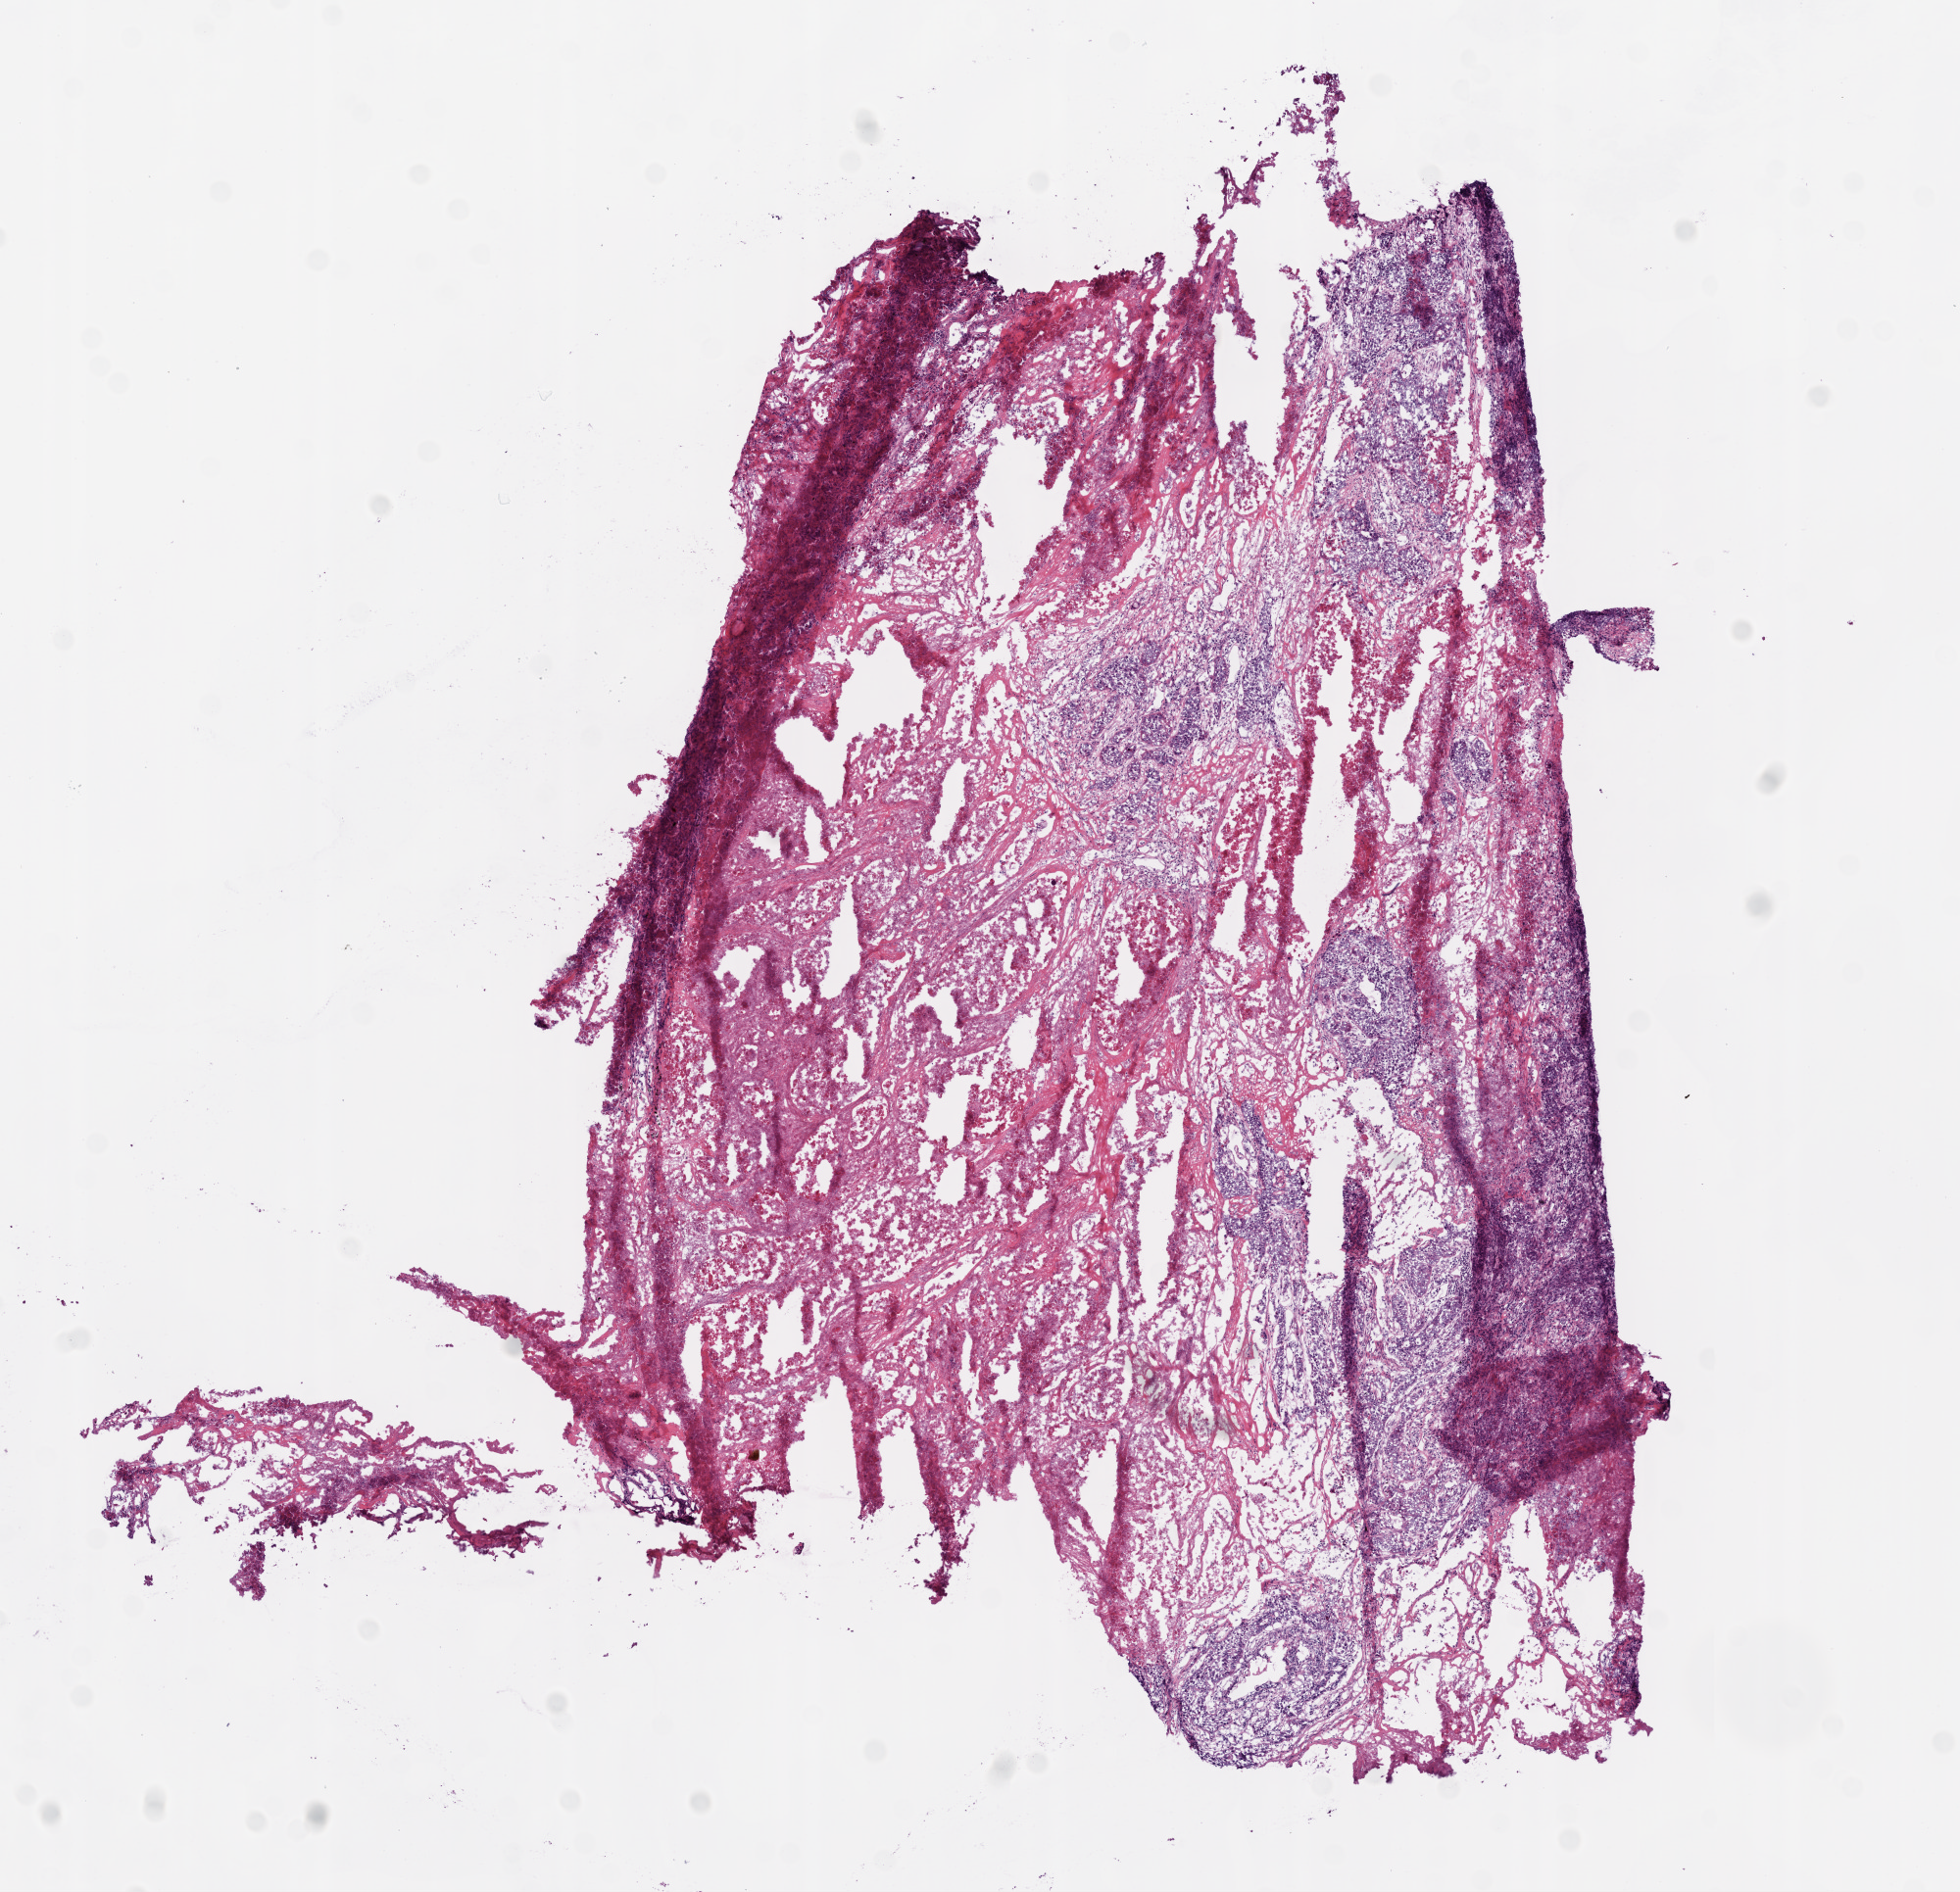
Digitized Hematoxylin and eosin (H&E) stained tissue section (whole slide), low-resolution overview of the scanned area, about 8.0 x 7.7 mm (slide scanned at 20x), frozen section, lung, primary tumour sample. Male, age 73 years at initial diagnosis. Pathologist review of this section (percent, as recorded): tumour cells 45%, tumour nuclei 74%, normal cells 0%, stromal cells 5%, necrosis 50%.
* diagnosis: Squamous cell carcinoma, NOS
* TNM: T2 N1 M0
* laterality: right
* AJCC pathologic stage: IIB (5th edition)